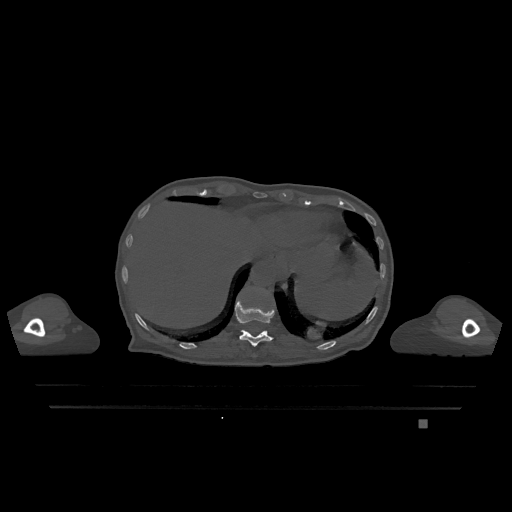
CT including the spine, one axial slice; slice 581 of 1317 in the series (ordered by position); bone window (W 1800 / L 400 HU); 0.5 mm slice thickness; 512 × 512 image matrix, field of view 500 × 500 mm. Female patient, age 74 years. From the clinical record (not read from this slice): primary cancer: lung; vertebrae with lytic lesions (as recorded): T1, T4, T5, T6, L4, L5.
Annotated regions visible in this slice (semi-automatically segmented with operator editing):
- T11 vertebra: box from (x=235, y=299) to (x=275, y=347) px